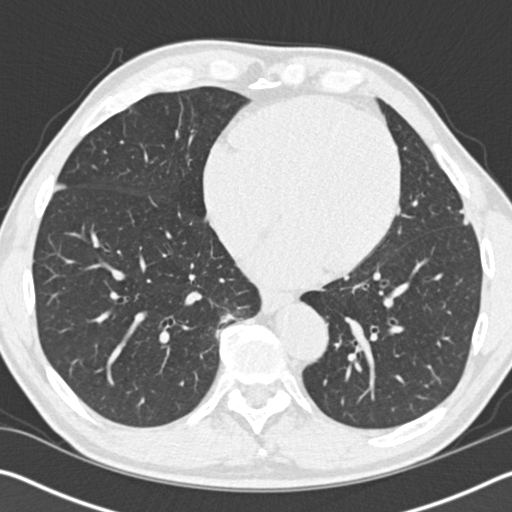
Low-dose screening chest CT, one axial slice. Slice 54 of 162 in the series (ordered by position). Reconstruction kernel B30f. Lung window (W 1500 / L -600 HU). 512 × 512 image matrix.
Structures marked on this image (expert manual segmentation):
- lesion 1 (tumor, upper lobe of left lung): bounding box [x1, y1, x2, y2] px = [459, 209, 469, 225]